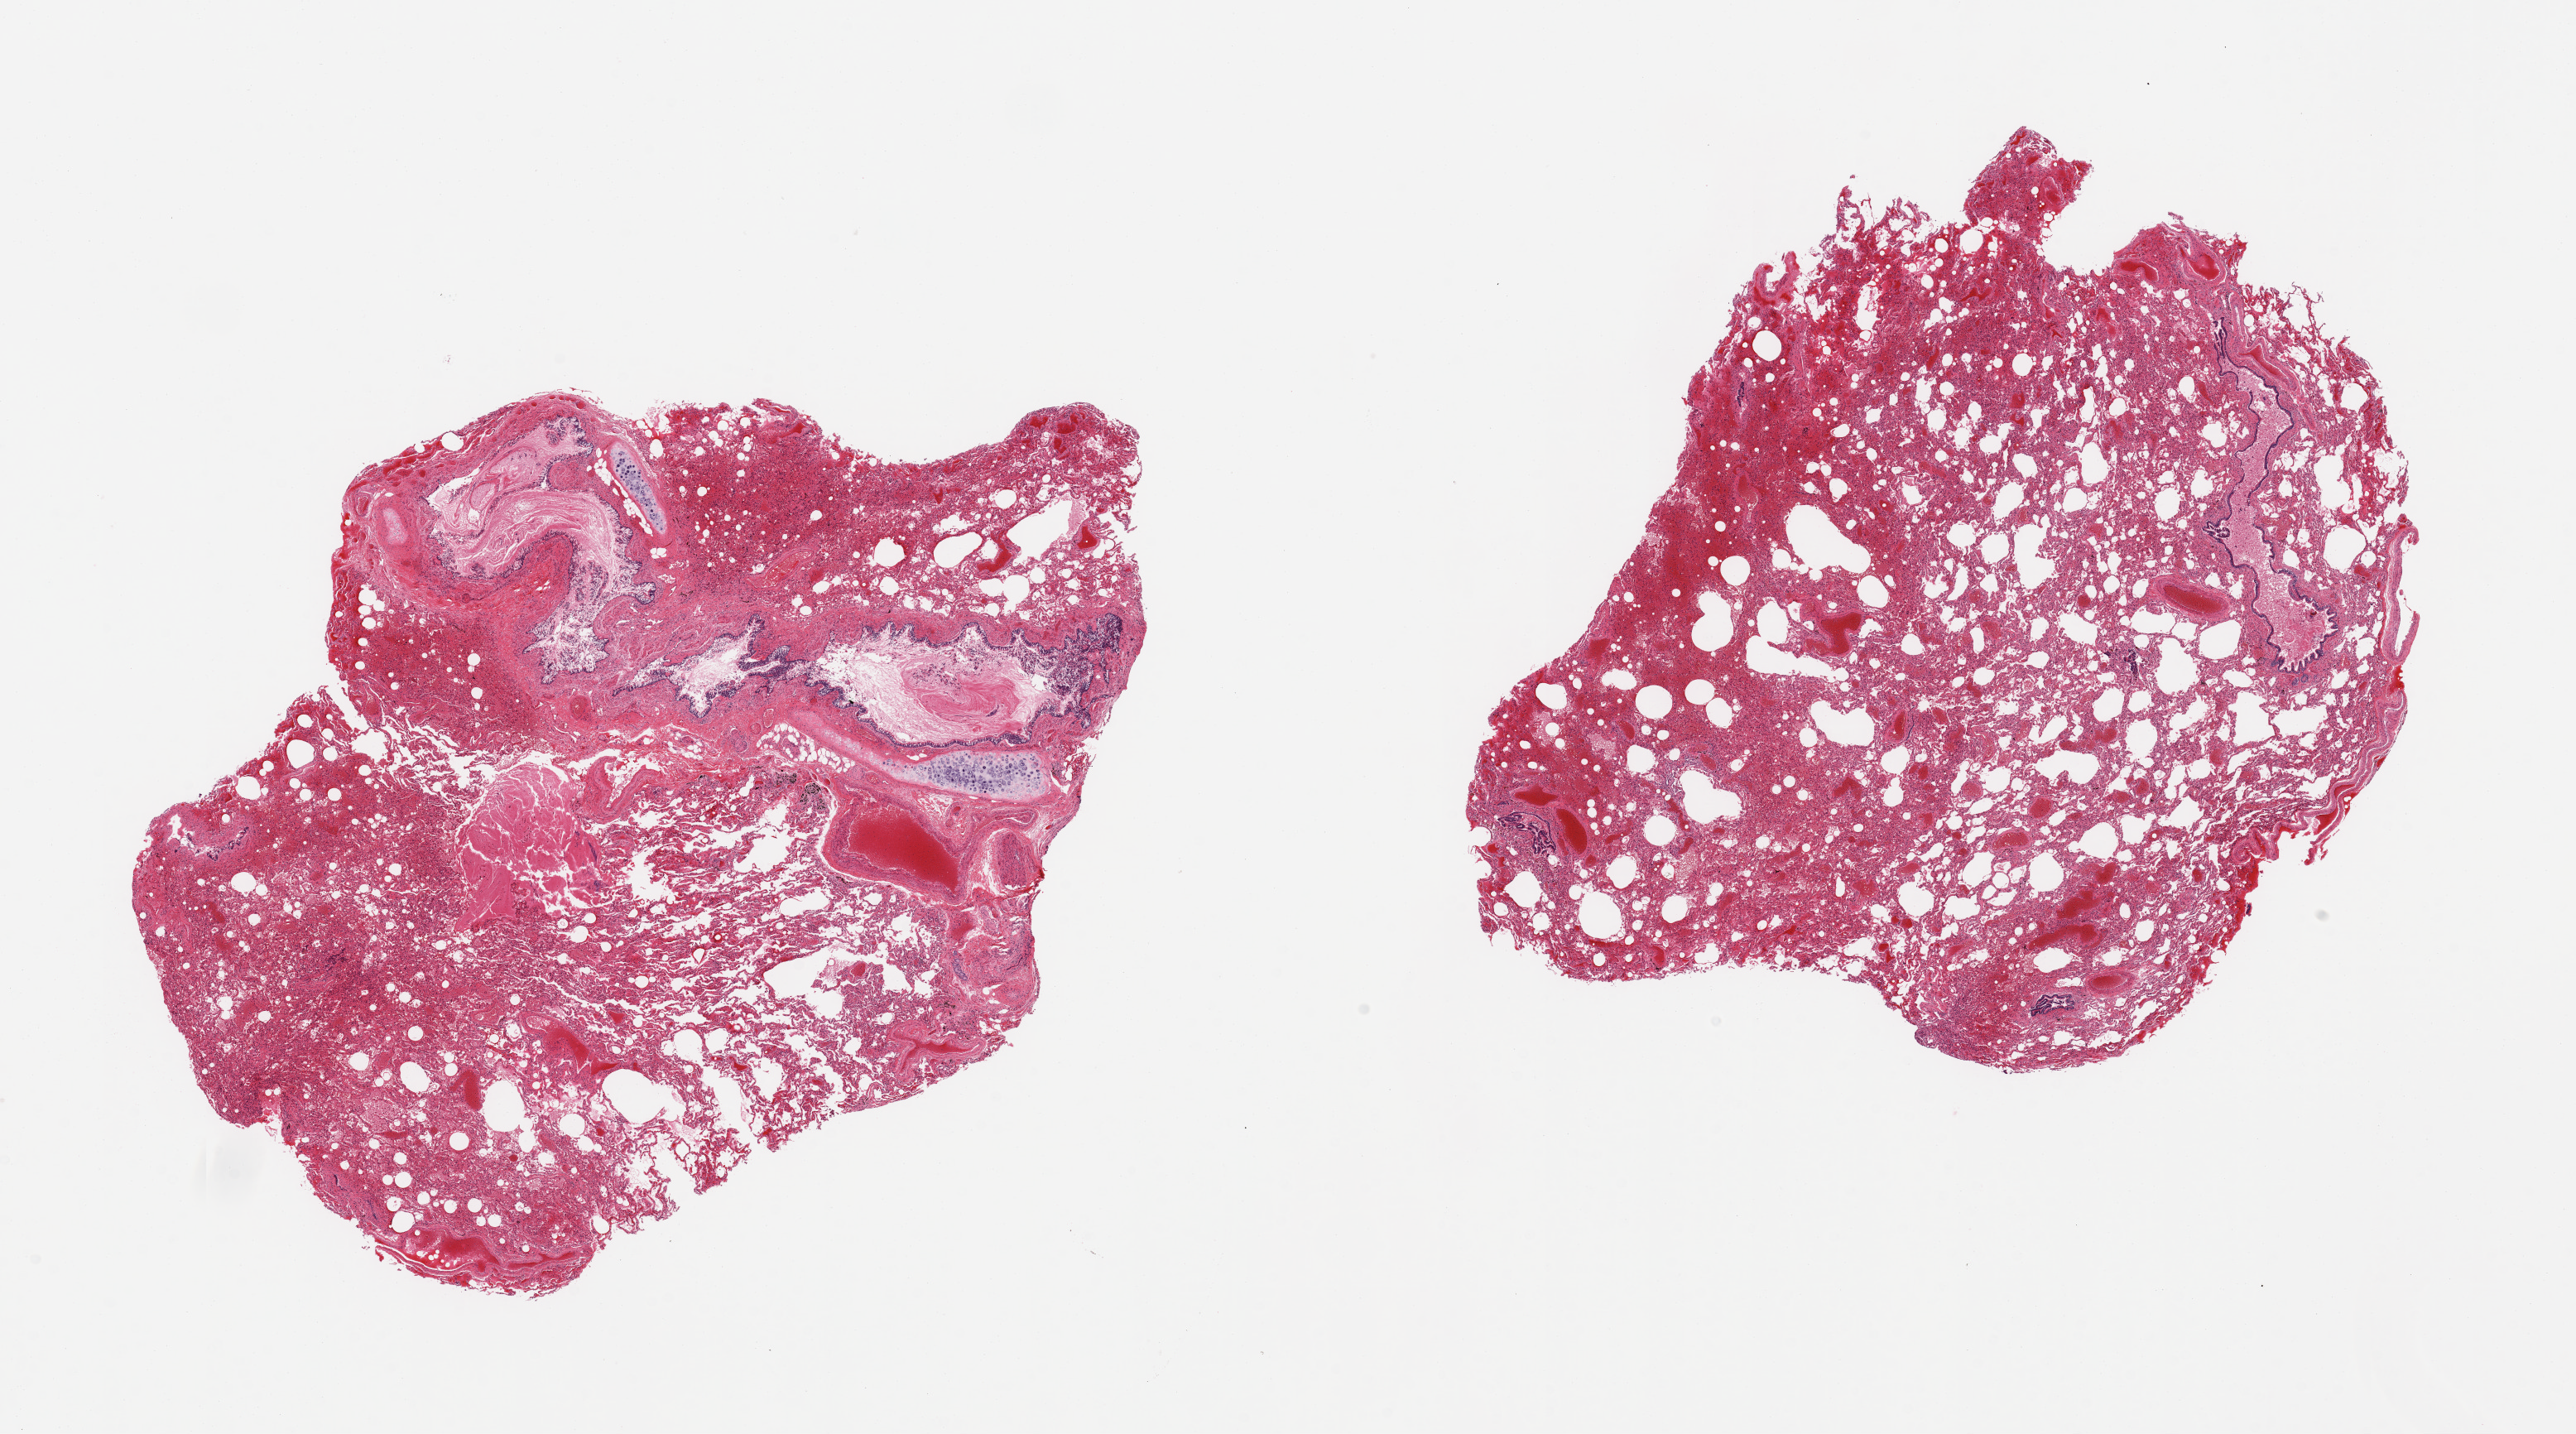
Digitized haematoxylin and eosin-stained section, shown as a low-resolution overview of the whole scanned area (about 24.6 x 13.7 mm, acquisition: 20x scan). PAXgene-fixed paraffin-embedded (PFPE) section. Target tissue: lung. Donor tissue sample. Male donor.
Review note (as recorded): 2 pieces, moderate congestion/chronic pneumonitis.